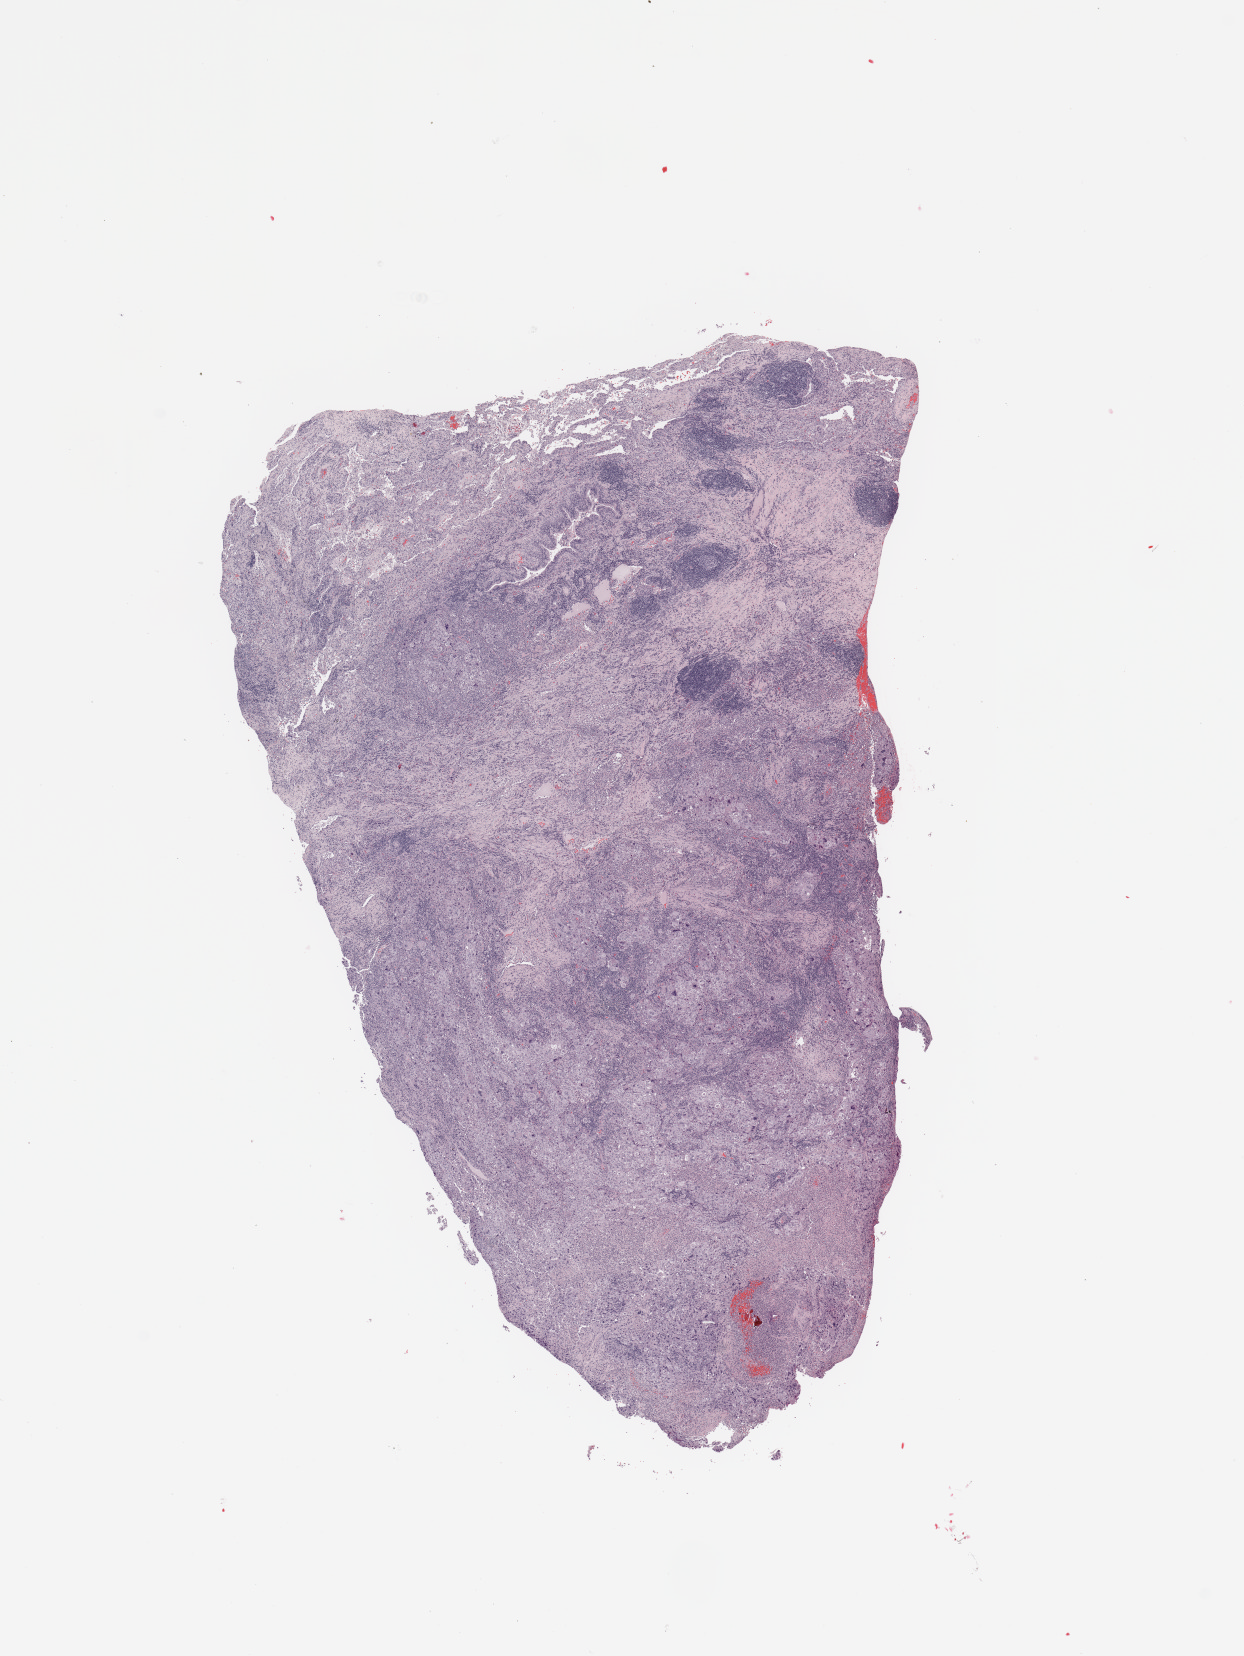
H&E-stained whole-slide image — low-resolution overview of the scanned area, about 9.8 x 13.1 mm (from a 20x scan), tumour tissue sample, sampled site: lung. Patient: female, age 66 years. Histologic grade: G3 (poorly differentiated). Composition of this section per pathologist review: tumour nuclei 70%, necrosis 10%.
AJCC pathologic stage: IIA. Diagnosis: Adenocarcinoma, NOS.